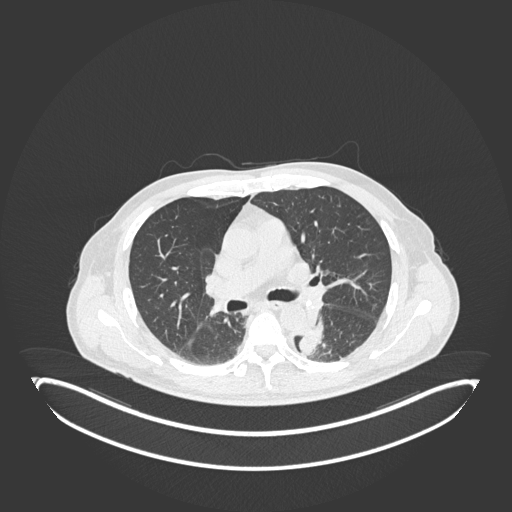
Chest CT, one axial slice. Position 125 of 251 along the scan axis. 120 kVp. Lung window (W 1500 / L -600 HU). 1 mm slice thickness. 512 × 512 image matrix. Male patient, age 72 years. Case-level facts recorded for this patient, not image findings: clinical TNM (as recorded): T2b N0 M1.
Outlined on this slice (rectangle marked by the reading radiologist):
- lung tumour (recorded histology: adenocarcinoma): bounding box <295,315,334,357> (left, top, right, bottom; pixels)